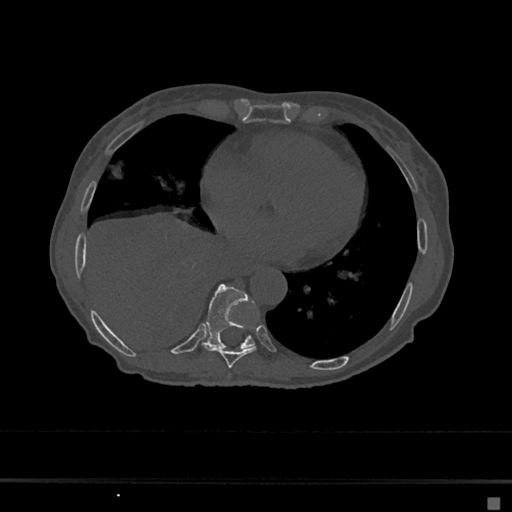
CT including the spine, one axial slice; slice 300 of 797 in the series (ordered by position); reconstruction kernel Br40s/3; bone window (W 1800 / L 400 HU); 0.5 mm slice thickness; 512 × 512 image matrix, field of view 360 × 360 mm. Female patient, age 68 years. Case-level facts recorded for this patient, not image findings: primary cancer: renal.
Annotated regions visible in this slice (semi-automatic segmentation, software-assisted and operator-edited):
- T8 vertebra: box from (x=207, y=327) to (x=257, y=368) px
- T9 vertebra: (x=203, y=283)–(x=255, y=349)